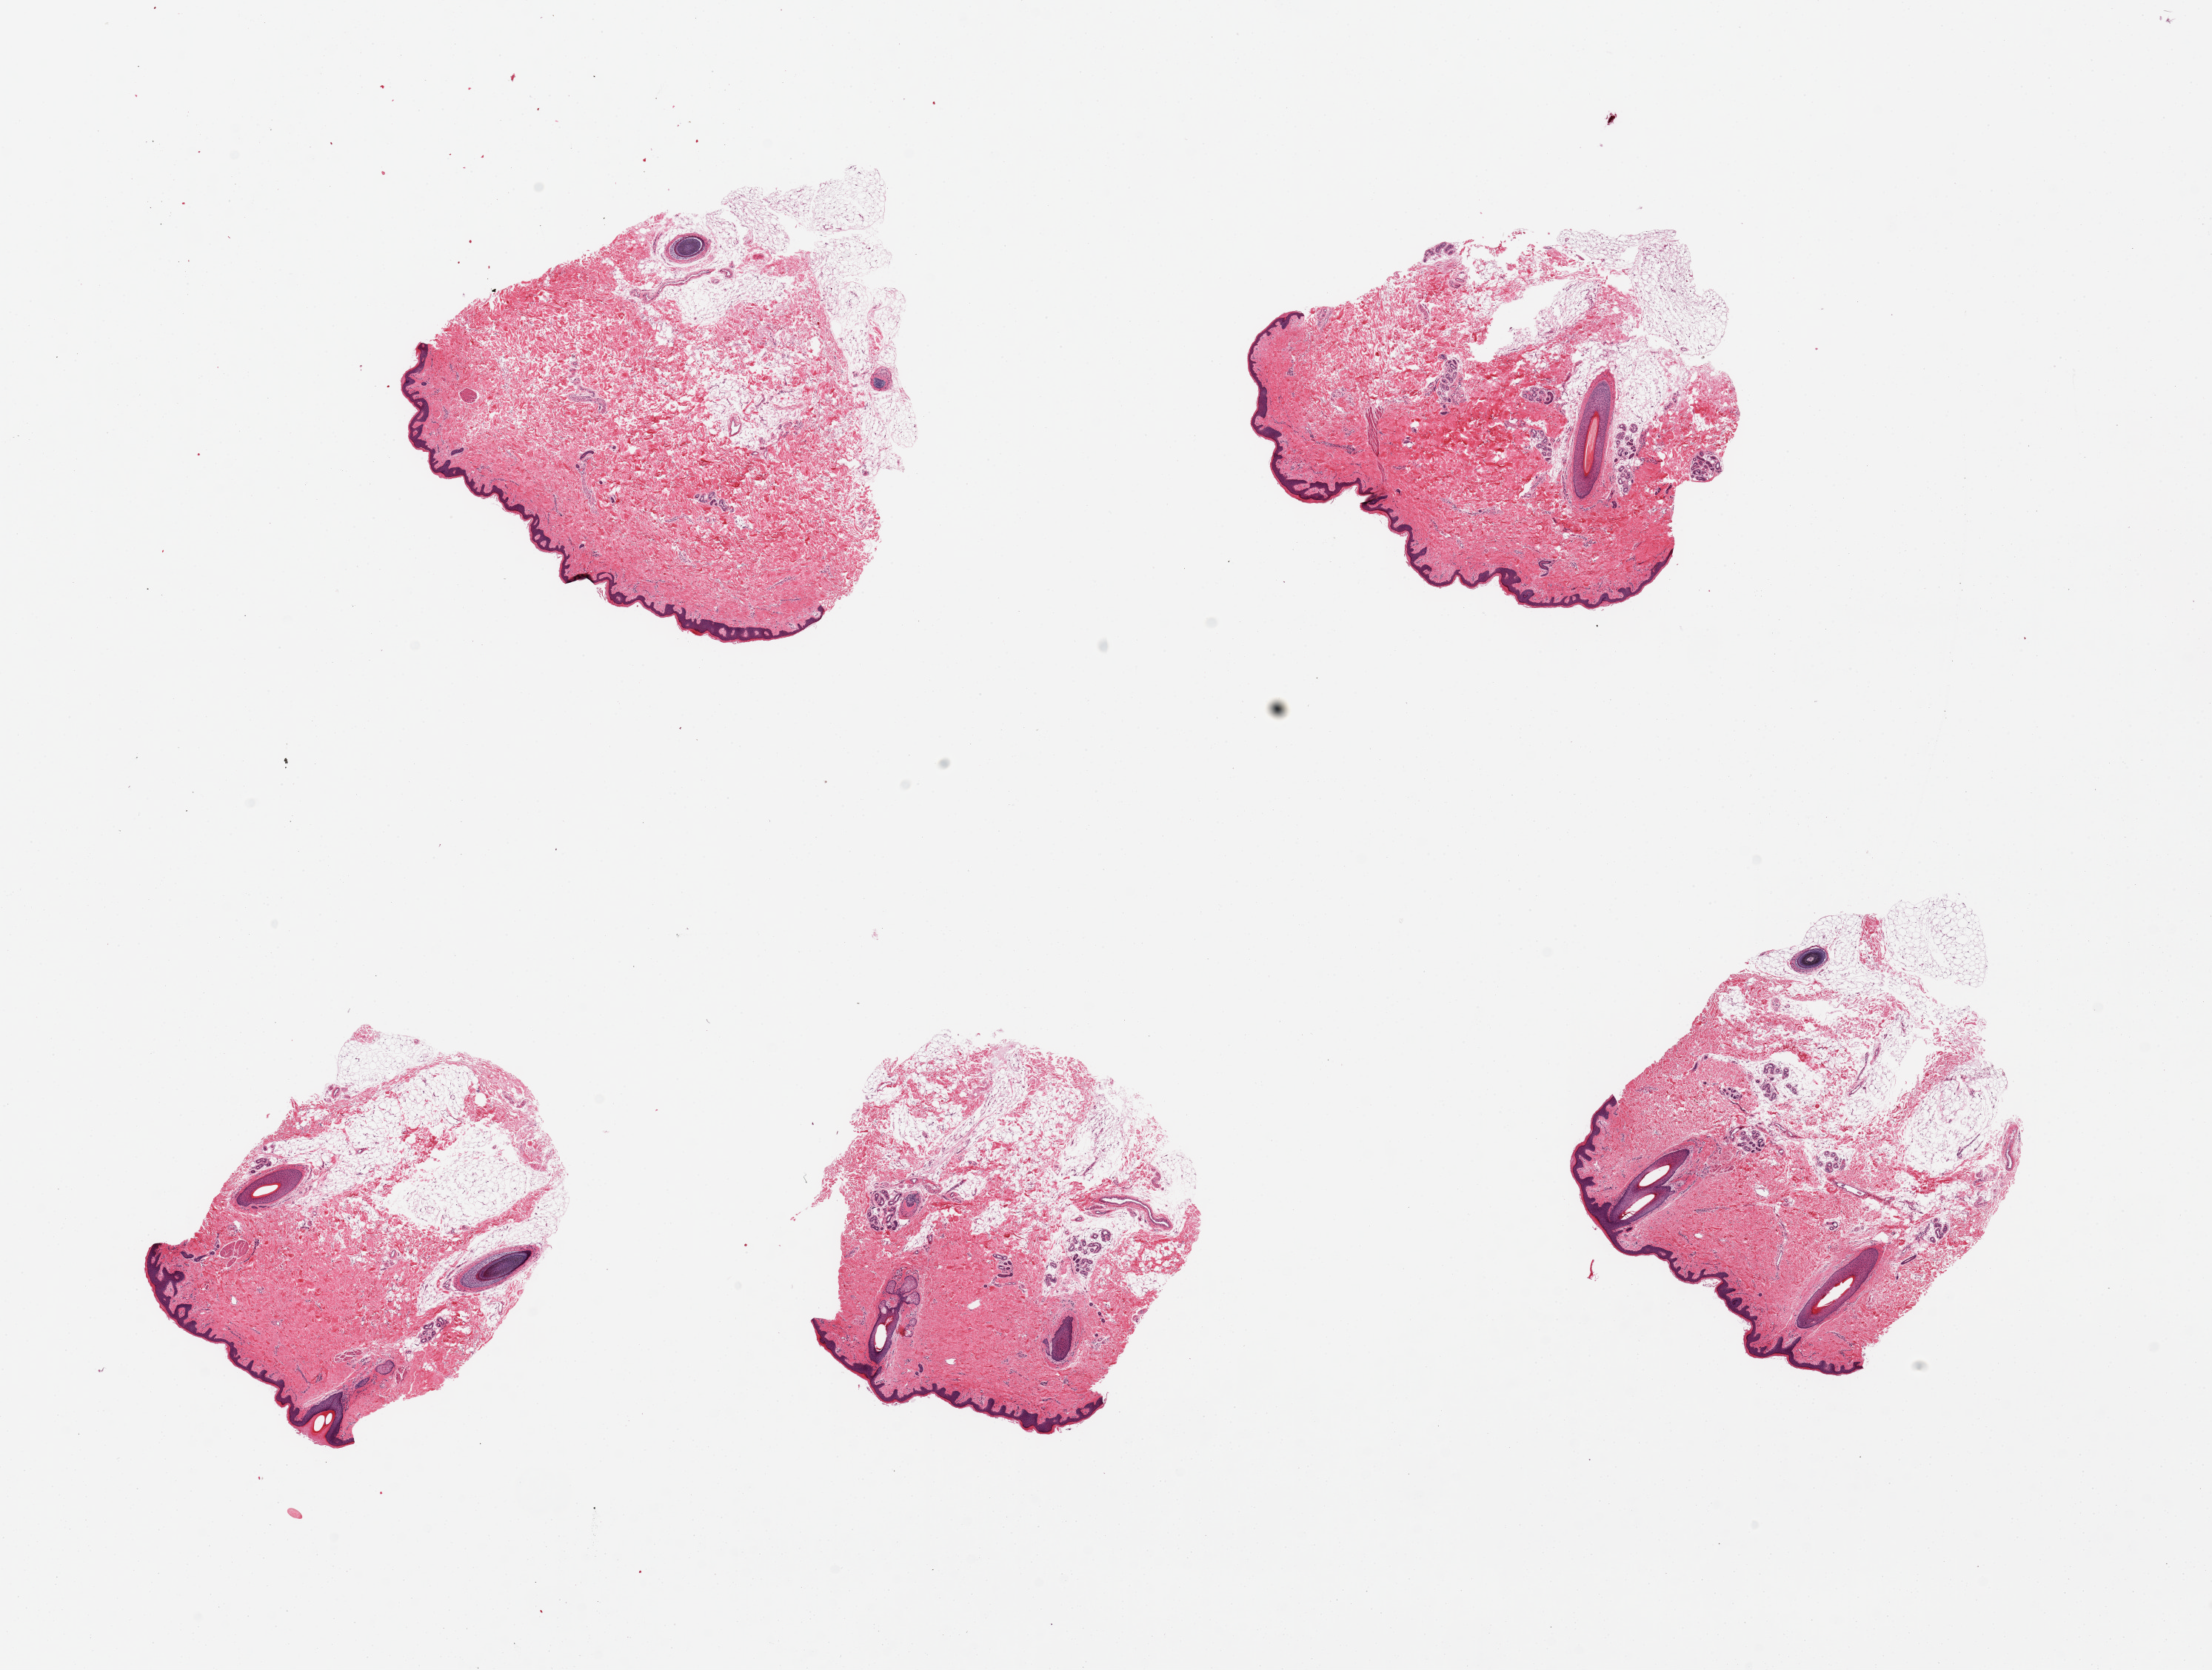
Whole-slide image, H&E stain, shown as a low-resolution overview of the whole scanned area (about 23.6 x 17.8 mm), PAXgene-fixed, paraffin-embedded tissue, section of skin of suprapubic region (target tissue), donor tissue sample.
Reviewer comment on this tissue sample: 5 pieces, 10-40% attached and internal fat.